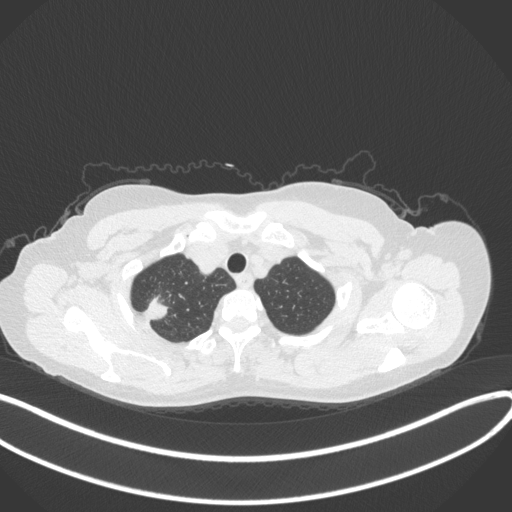
Chest CT, one axial slice; 120 kVp; lung window (W 1500 / L -600 HU); 1 mm slice thickness; 512 × 512 image matrix, field of view 400 × 400 mm. Patient: female, 50 years. Case-level facts recorded for this patient, not image findings: clinical TNM (as recorded): T1c N0 M0; histopathological grade: G2-3.
Structures marked on this image (bounding box drawn by a radiologist):
- lung tumour (recorded histology: adenocarcinoma): box from (x=141, y=297) to (x=169, y=321) px